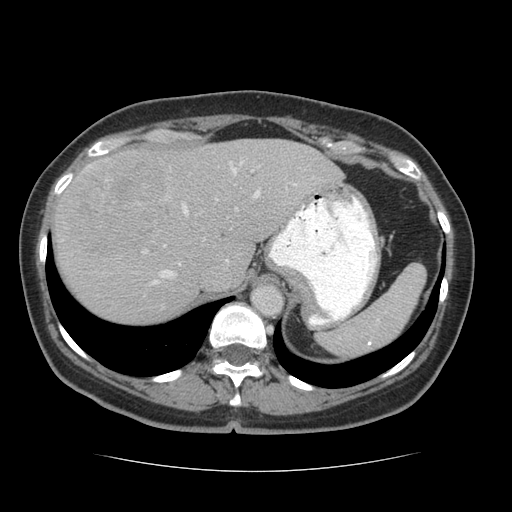
Contrast-enhanced abdominal CT (liver protocol), one axial slice; position 50 of 75 along the scan axis; reconstruction kernel STANDARD; 140 kVp; soft-tissue window (W 400 / L 40 HU); 512 × 512 image matrix. From the clinical record (not read from this slice): diagnosis: hepatocellular carcinoma (patient treated with transarterial chemoembolisation; whether this scan precedes or follows treatment is not stated here); TNM stage (as recorded): Stage-I; Child-Pugh class: A; tumour differentiation: moderately differentiated; tumour nodularity: uninodular.
Outlined on this slice (semi-automatically segmented with operator editing):
- abdominal aorta: bounding box <252,285,282,315> (left, top, right, bottom; pixels)
- liver parenchyma outside the tumour (the mass and vessels are separate outlines, so this box may not span the whole liver): <52,138,343,322>
- mass: <62,151,175,255>
- liver vessels: <58,161,297,285>